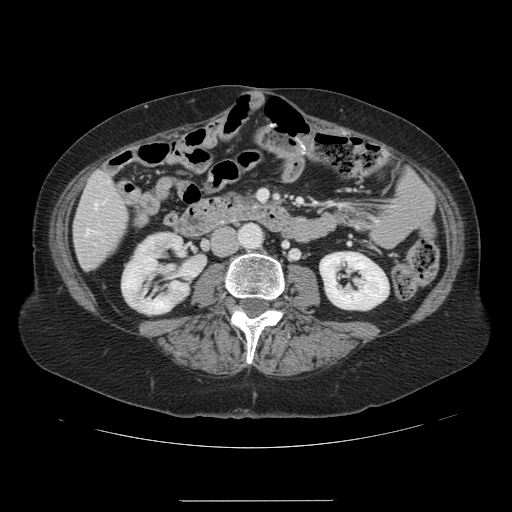
Contrast-enhanced abdominal CT, one axial slice; slice 28 of 141 in the series (ordered by position); soft-tissue window (W 400 / L 40 HU); 2.5 mm slice thickness; 512 × 512 image matrix, field of view 393 × 393 mm. Female patient, age 74 years. From the clinical record (not read from this slice): diagnosis: colorectal cancer liver metastases, imaged before liver resection; multiple liver metastases: yes; largest metastasis: 7 cm; disease in both lobes: yes.
Annotated regions visible in this slice (manually delineated by an expert):
- hepatic veins: bounding box <86,203,97,234> (left, top, right, bottom; pixels)
- liver: <75,173,128,269>
- planned liver remnant (the part of the liver to remain after resection): <75,173,126,269>